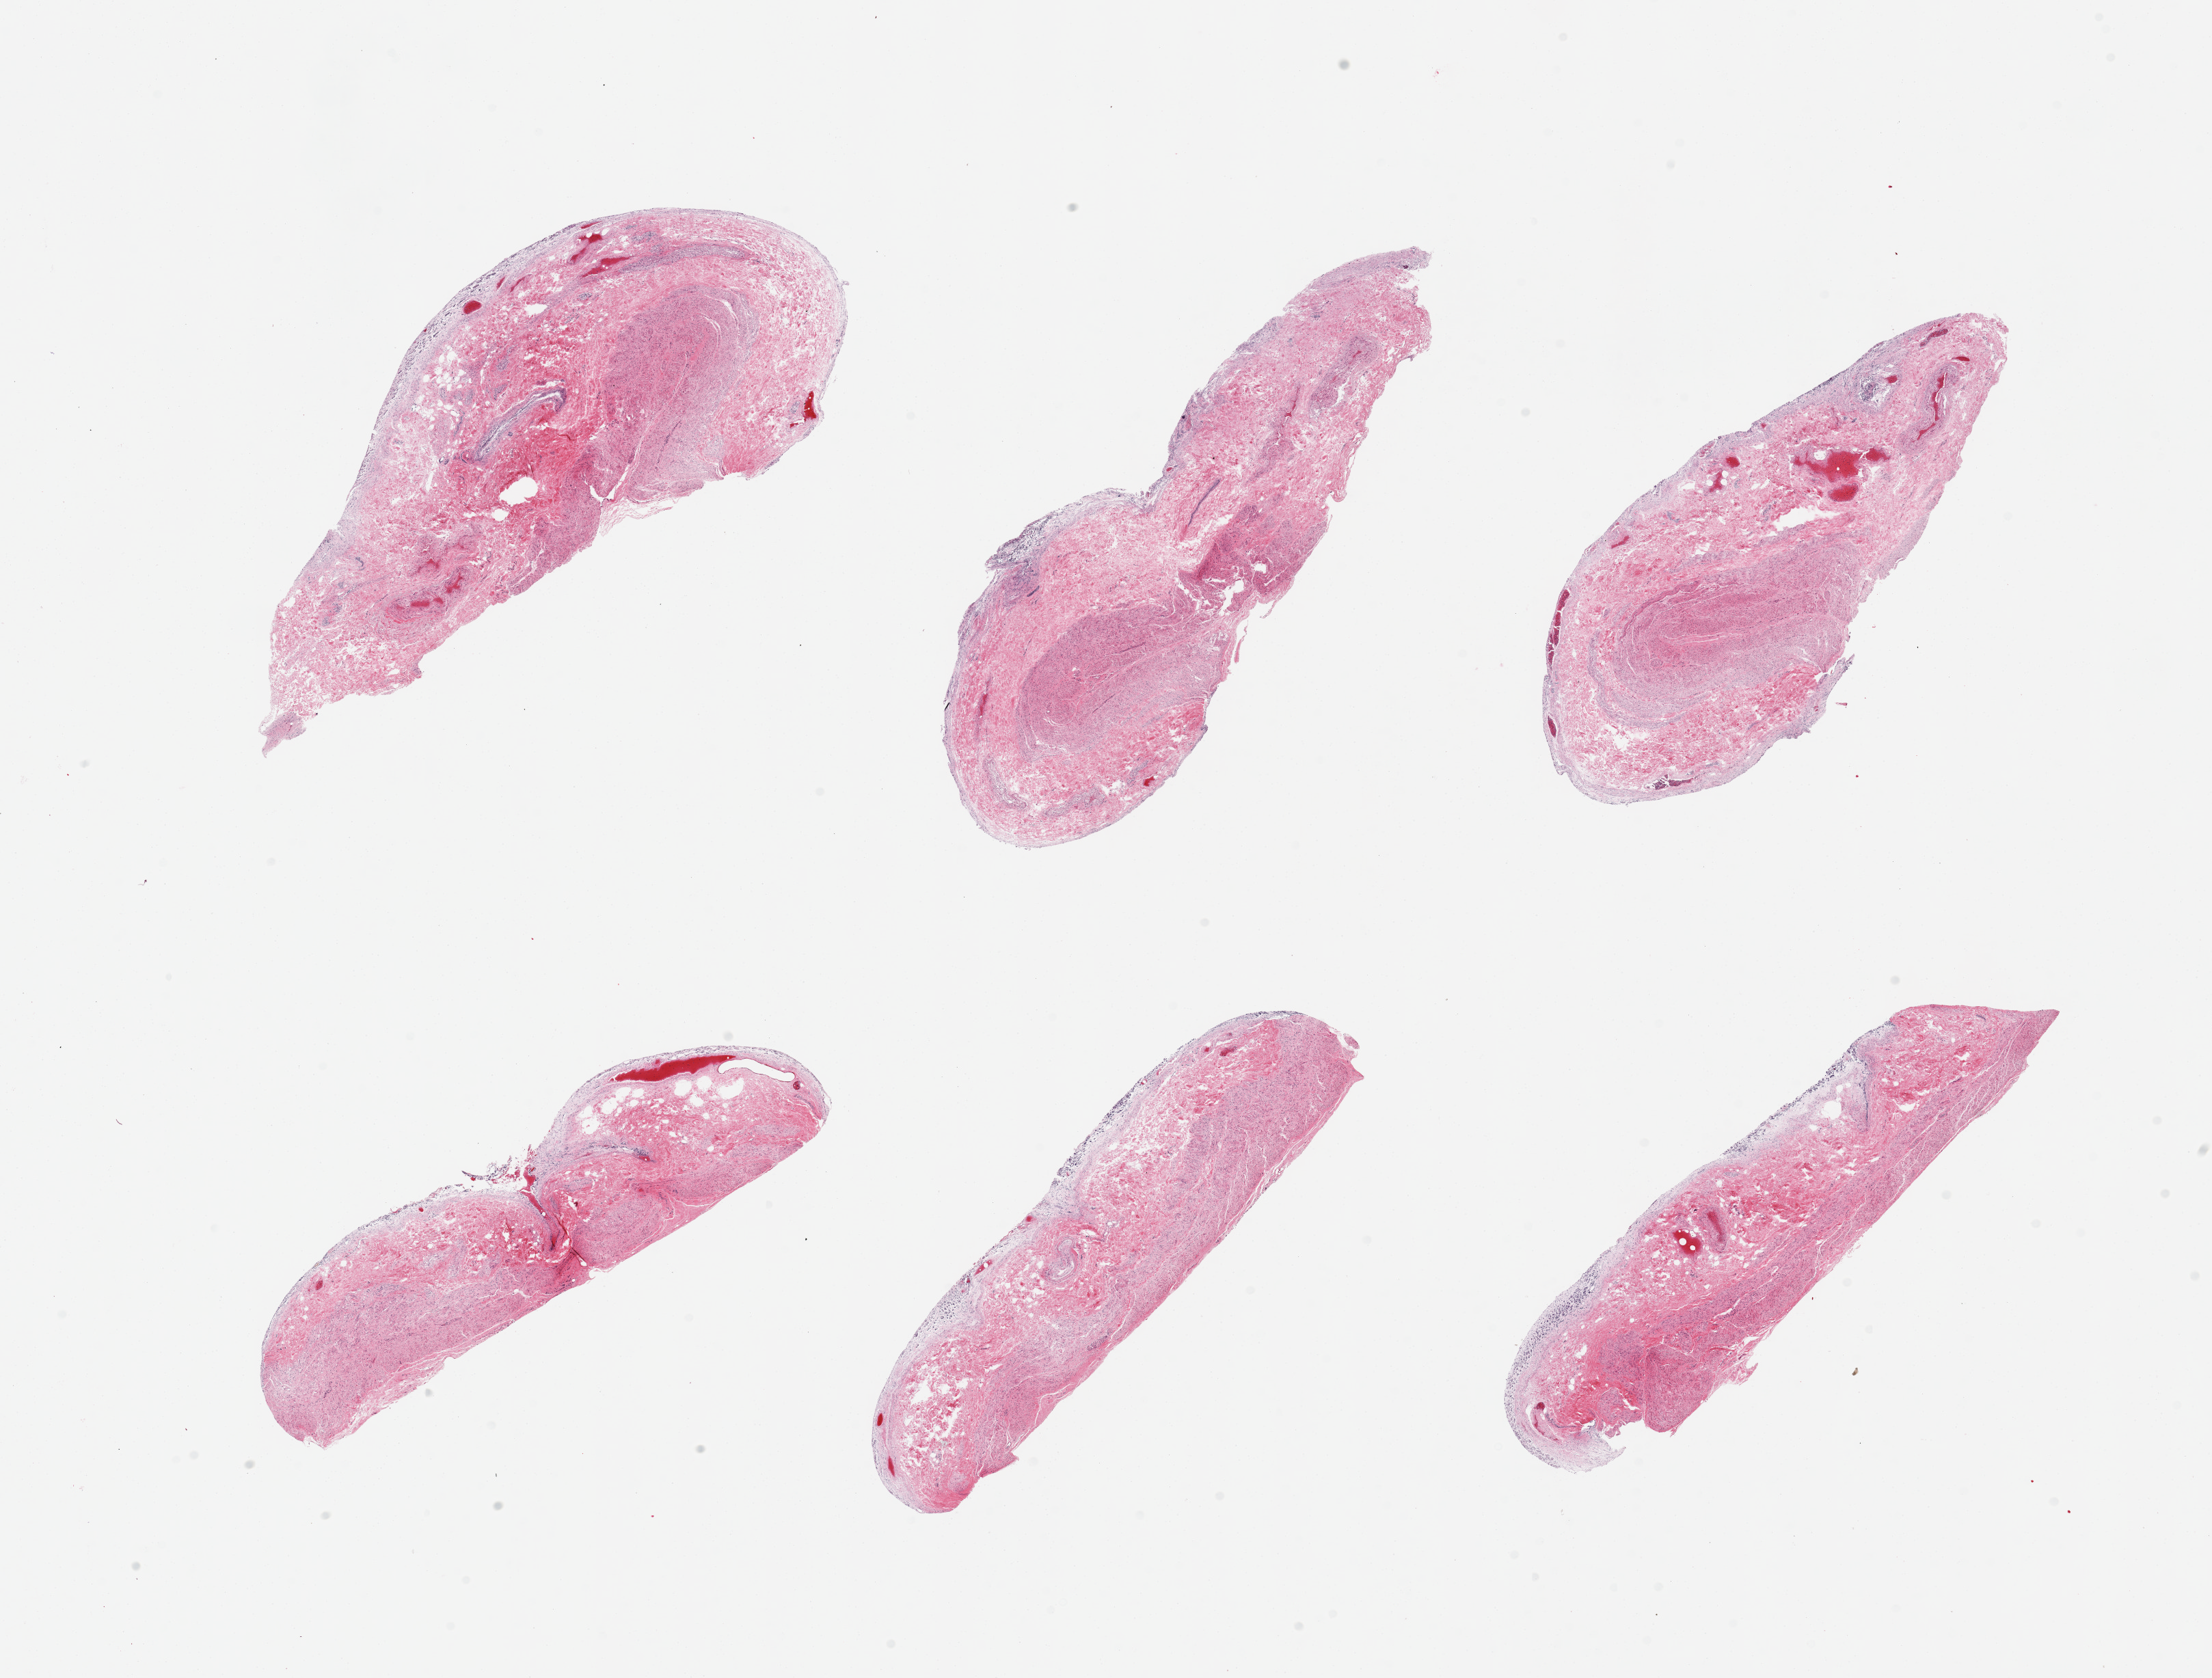
Digitized haematoxylin and eosin-stained section, brightfield — a low-resolution overview of the entire scanned area, about 25.6 x 19.4 mm; PAXgene-fixed, paraffin-embedded tissue; target tissue: stomach; tissue donor sample. Male donor.
Review note (as recorded): 6 pieces; totally autolyzed mucosa; poorly preserved muscularis.